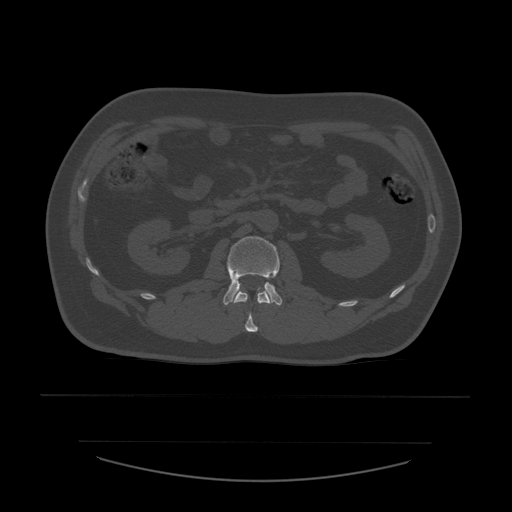
CT including the spine, one axial slice. Position 210 of 532 along the scan axis. Bone window (W 1800 / L 400 HU). 1.25 mm slice thickness. 512 × 512 image matrix. Patient age 44 years. From the clinical record (not read from this slice): primary cancer: soft tissue sarcoma.
Structures marked on this image (semi-automatically segmented with operator editing):
- L1 vertebra: bounding box (x1, y1, x2, y2) in pixels: (233, 290, 275, 332)
- L2 vertebra: (223, 237, 283, 306)